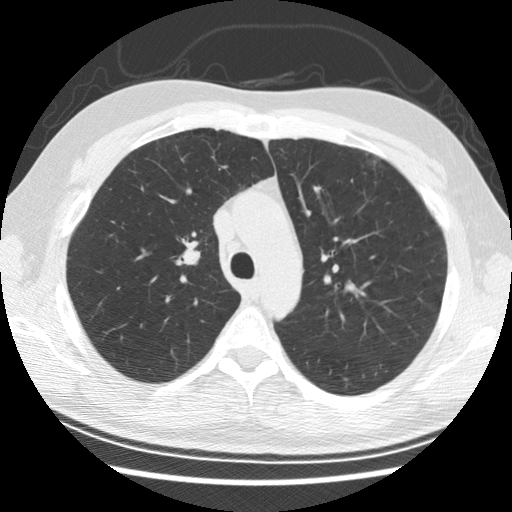
Axial slice from a low-dose chest CT screening exam. Baseline screening round. Lung window (W 1500 / L -600 HU). Standard (soft-tissue) reconstruction kernel (STANDARD). 120 kVp. Slice 84 of 278 in the series. 512 × 512 image matrix. Male participant, aged 57 years at enrolment. Former smoker at enrolment.
Lesion marked by an expert reader, bounding box [x1, y1, x2, y2] px = [163, 221, 220, 281]. The screening reader recorded 6 non-calcified nodules or masses ≥4 mm on this exam; which of them this box marks is not recorded. Official screen result: negative screen, minor abnormalities not suspicious for lung cancer. Participant outcome: lung cancer diagnosed 766 days after this screen (after the second annual screen) — adenocarcinoma, NOS, right upper lobe, poorly differentiated (G3), stage IB (AJCC 6th edition), 25 mm at pathology.